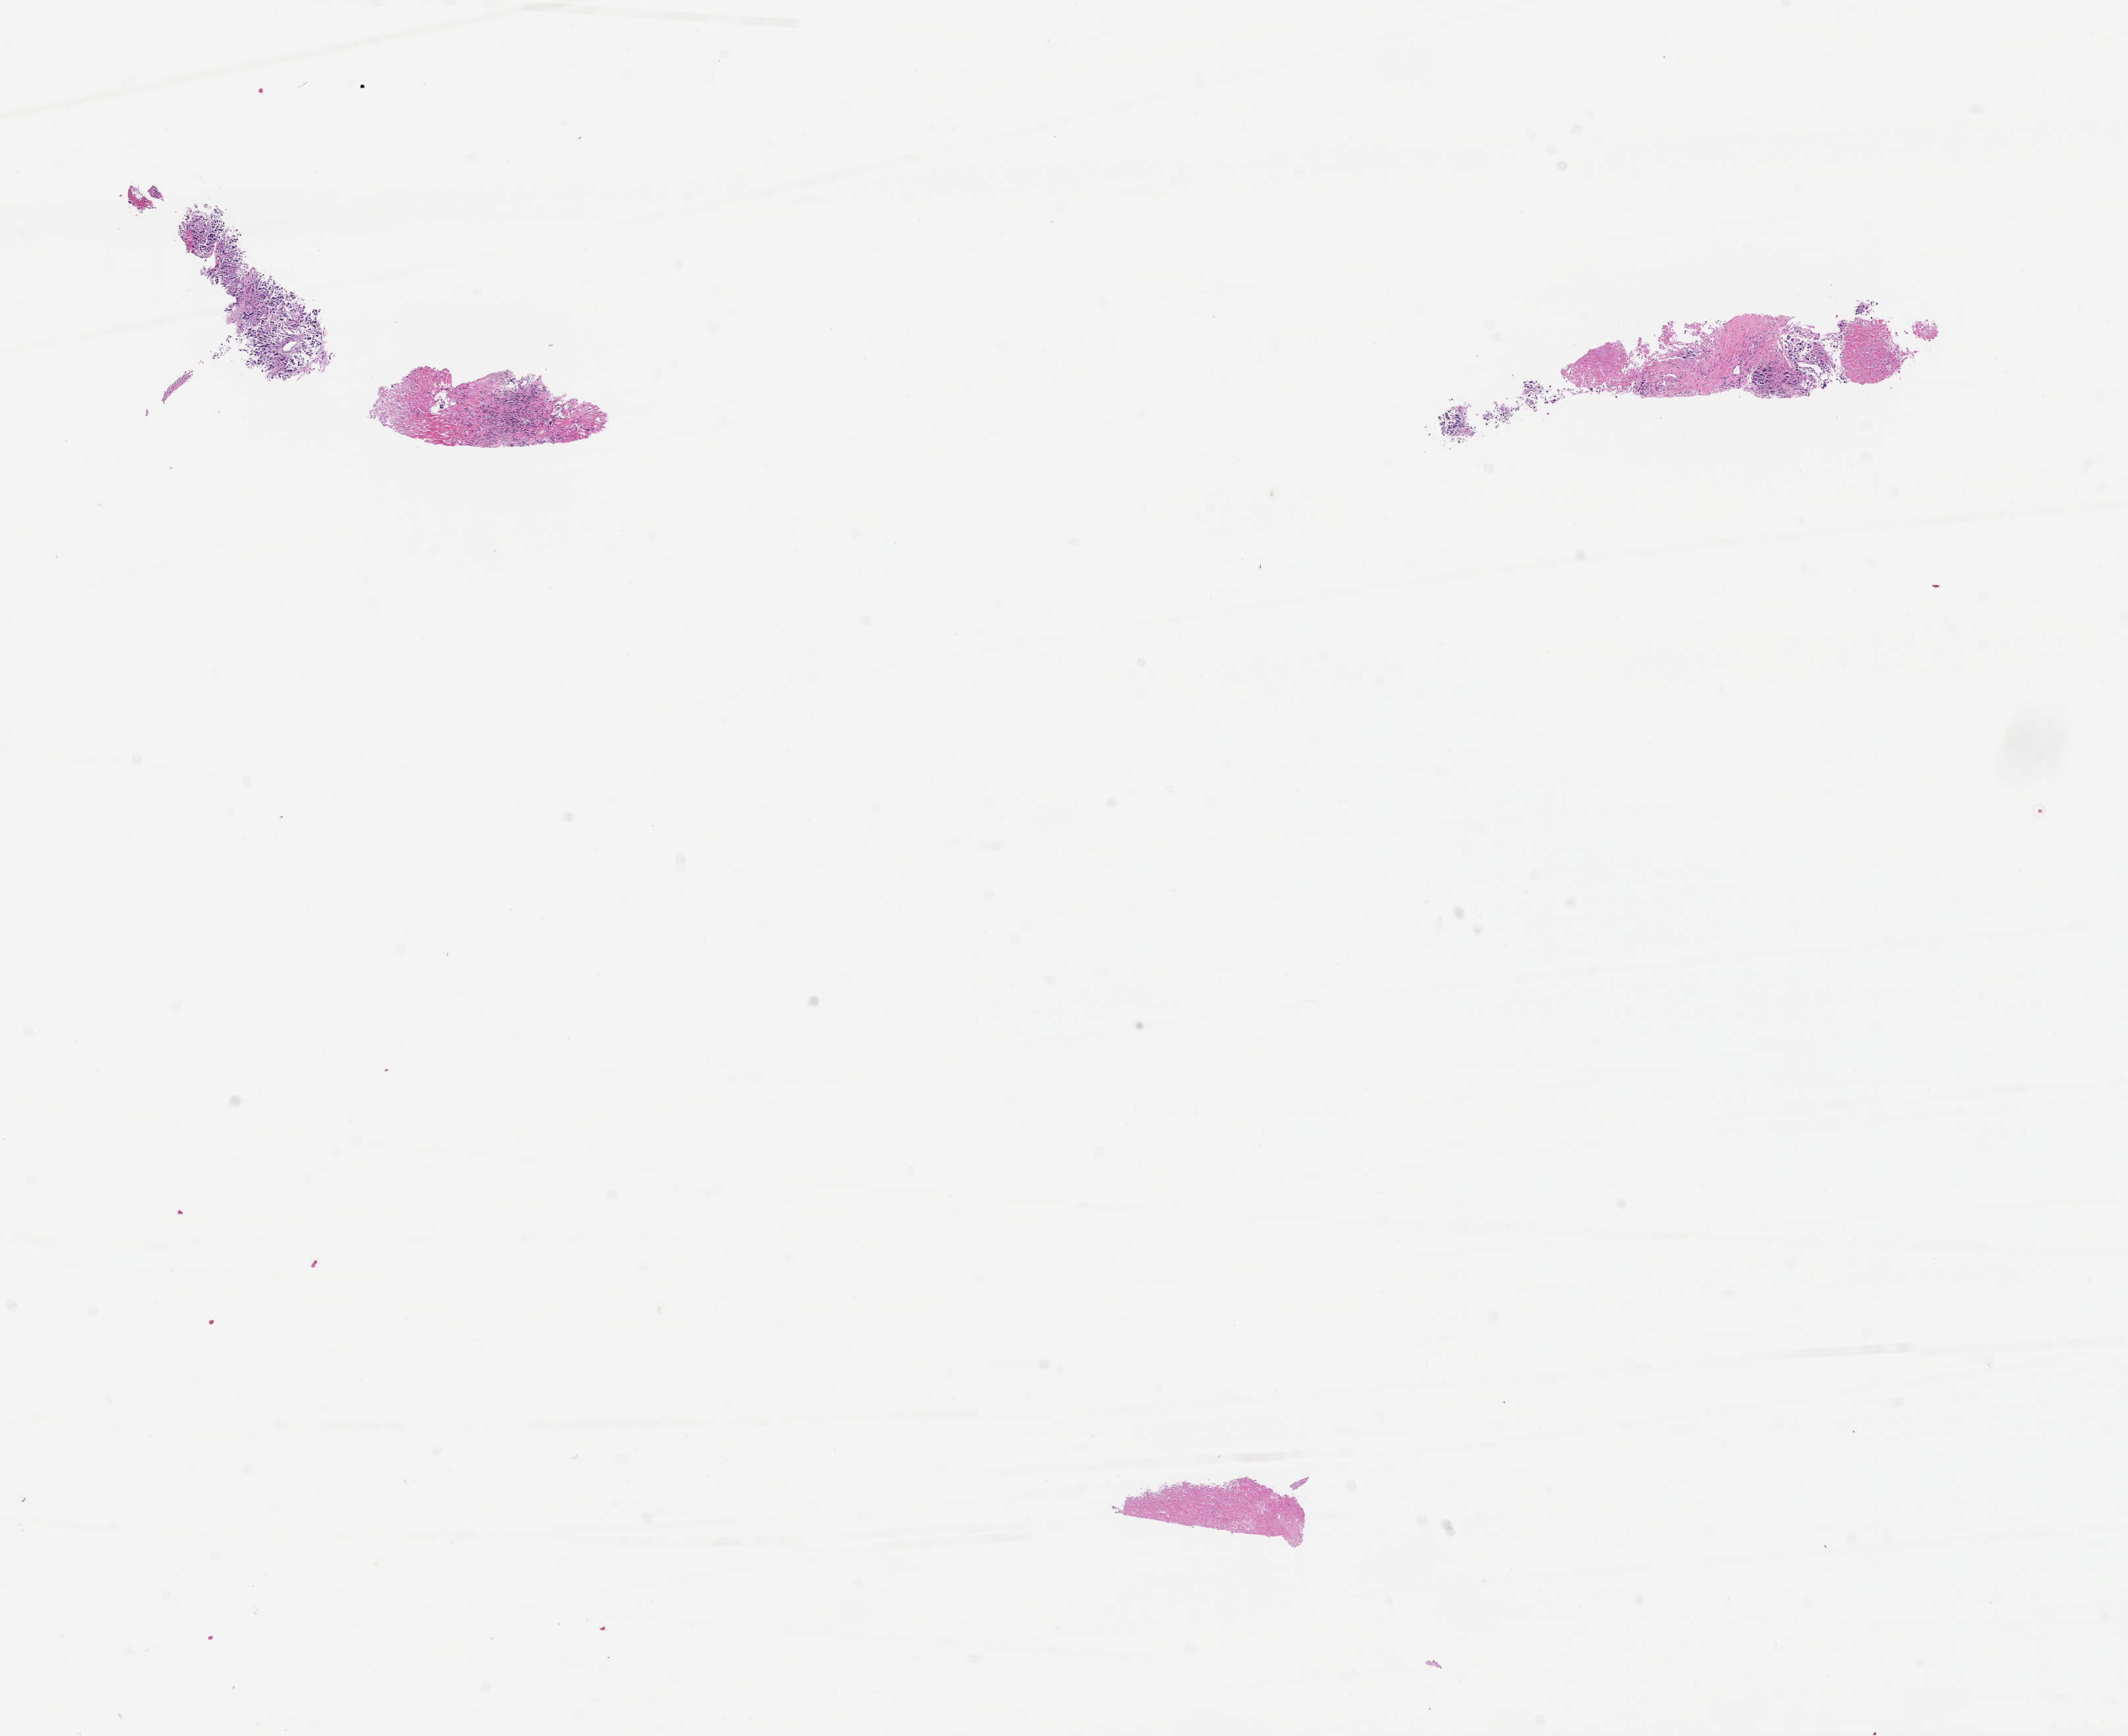
Whole-slide image, H&E stain — low-resolution overview of the scanned area, about 13.1 x 10.7 mm, FFPE section. Patient: male.
This section: metastasis (sampled organ not recorded). Primary diagnosis of the patient: Non-Small Cell Lung Carcinoma.